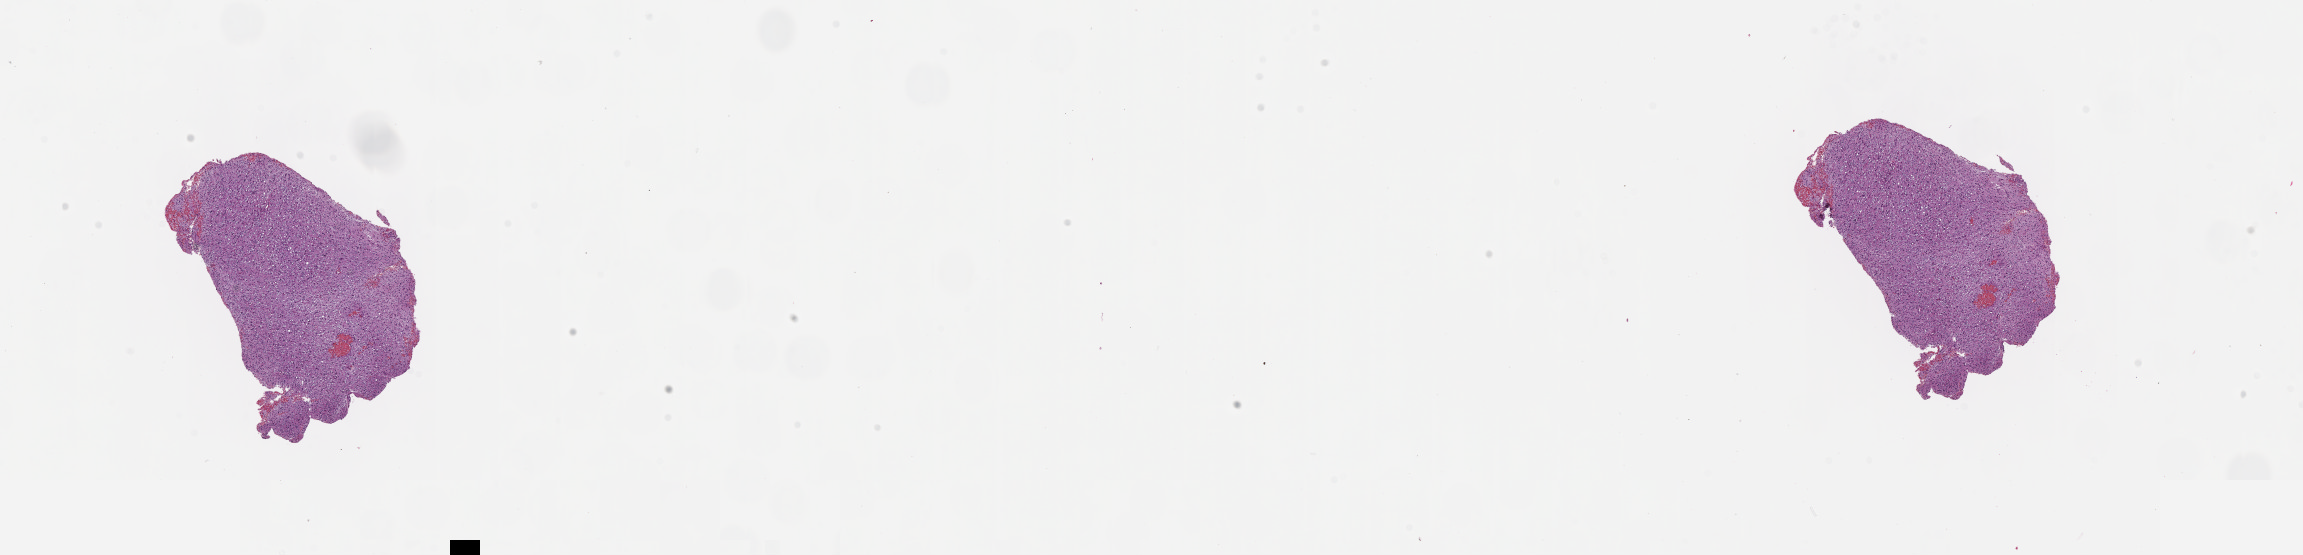
H&E-stained whole-slide image — a low-resolution overview of the entire scanned area, about 18.6 x 4.5 mm (from a 40x scan); formalin-fixed paraffin-embedded (FFPE) diagnostic section; primary tumour sample from the brain. Patient: male, age at initial diagnosis 30 years. Histologic grade: G2 (moderately differentiated).
• histologic diagnosis: Astrocytoma, NOS (cerebrum)